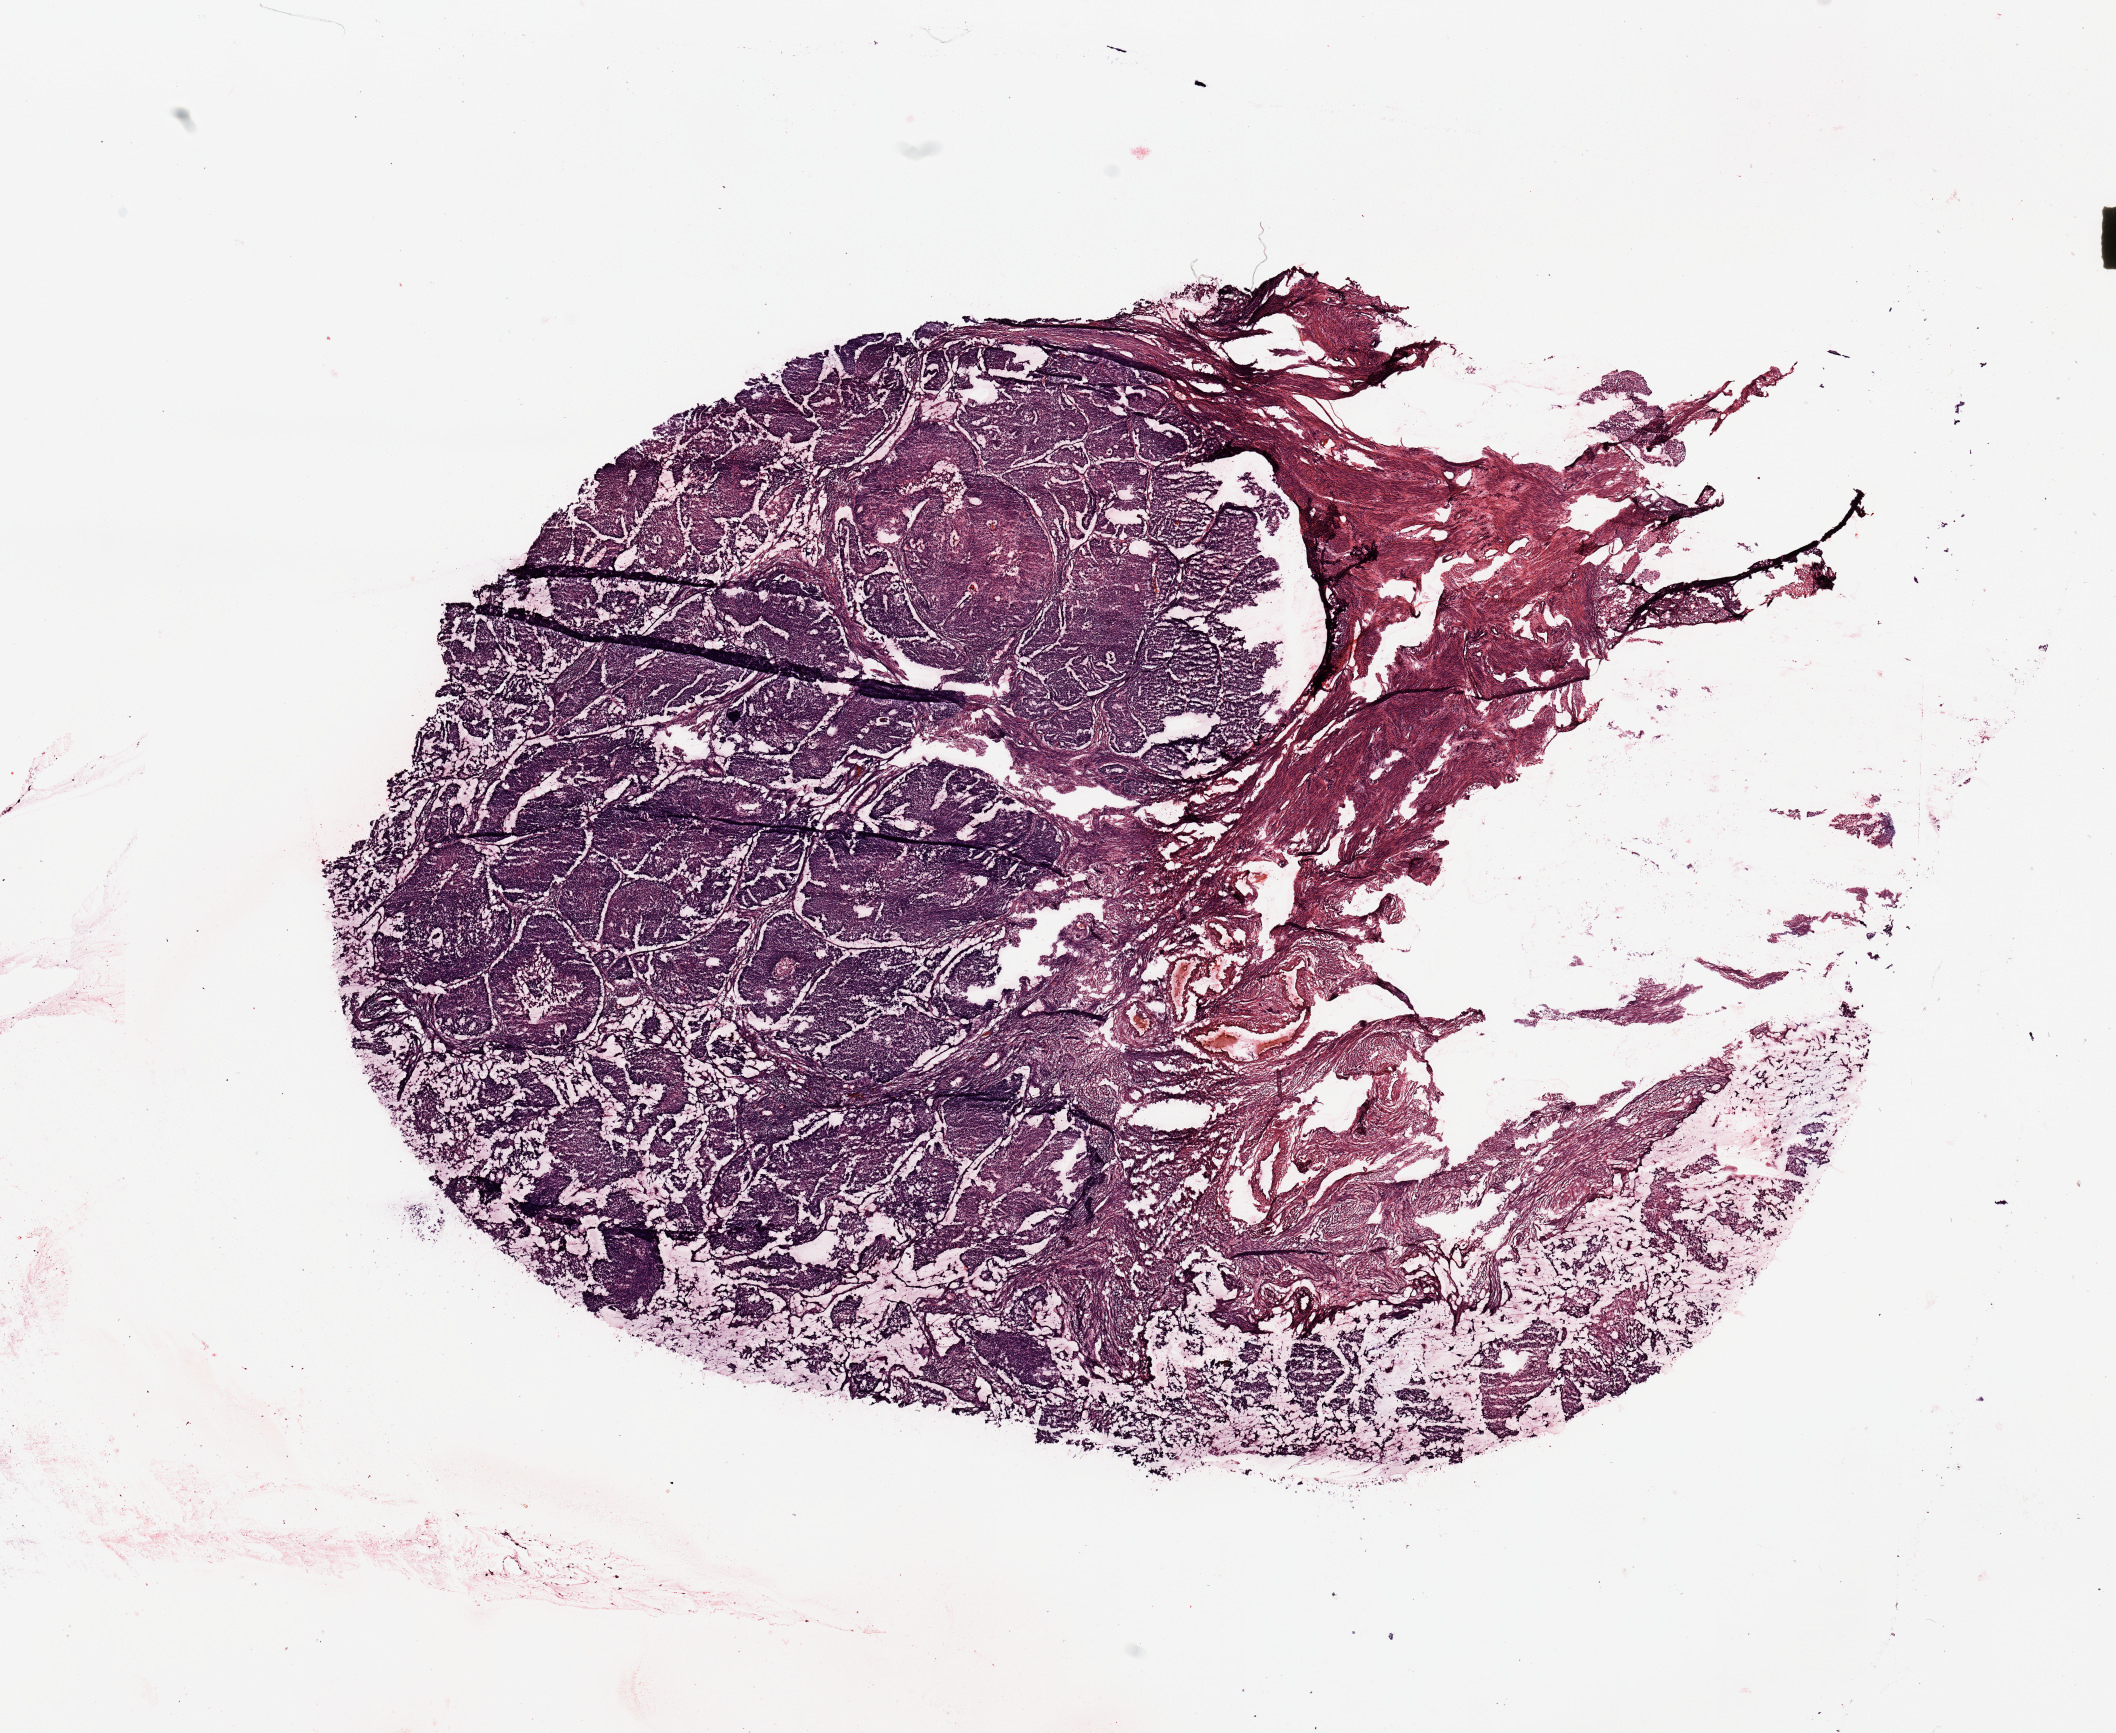
Digitized H&E tissue section (whole slide) — a low-resolution overview of the entire scanned area, about 16.7 x 13.7 mm (from a 20x scan), uterus, tumour tissue. 45-year-old female patient. Histologic grade: G2 (moderately differentiated).
AJCC pathologic stage: I. Diagnosis: Endometrioid adenocarcinoma, NOS.